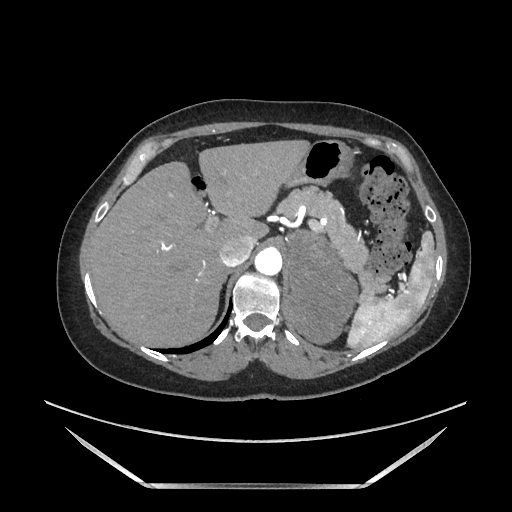
Contrast-enhanced abdominal CT, one axial slice; soft-tissue window (W 400 / L 40 HU); 1.25 mm slice thickness; 512 × 512 image matrix. Female patient. From the clinical record (not read from this slice): diagnosis: adrenocortical carcinoma; tumour side: left adrenal; tumour size at pathology: 12.5 cm; Ki-67 index: 39 %; stage (as recorded): 3.
Annotated regions visible in this slice (semi-automatic segmentation, software-assisted and operator-edited):
- mass: bounding box (x1, y1, x2, y2) in pixels: (287, 233, 356, 343)